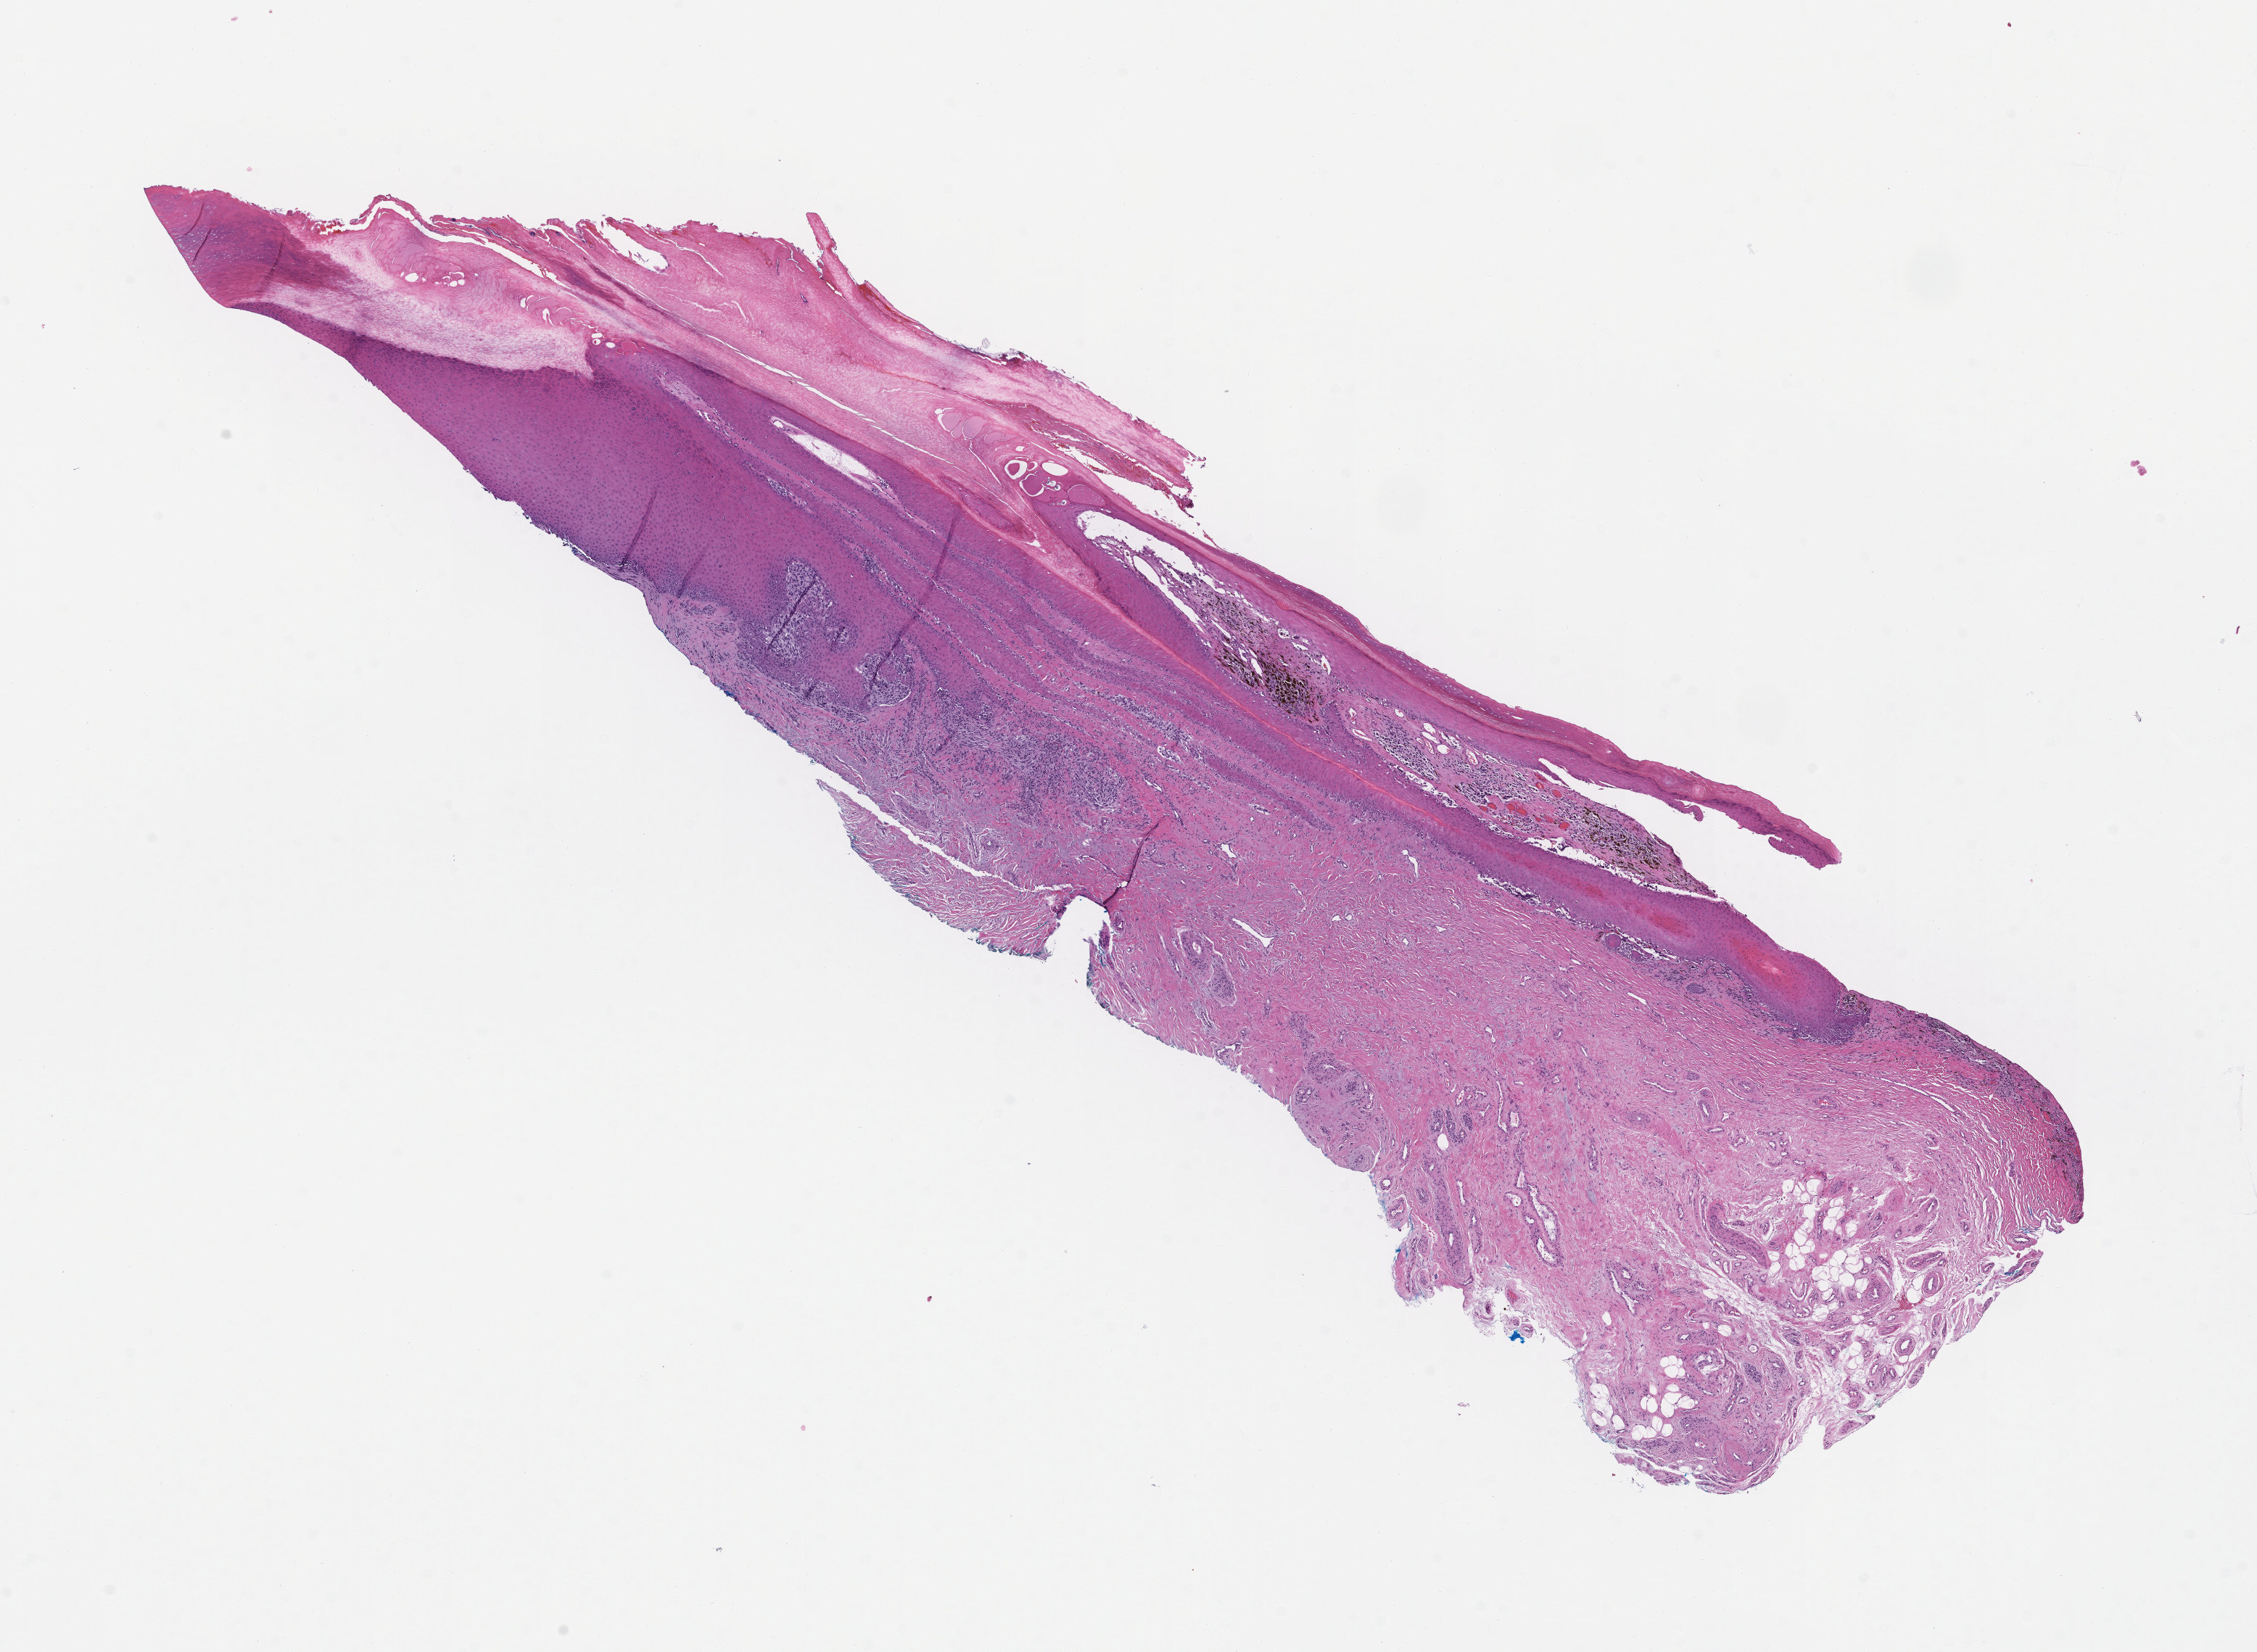
Whole-slide image, haematoxylin and eosin stain, whole scanned area (about 12.6 x 9.2 mm) shown as a low-resolution overview; formalin-fixed, paraffin-embedded (FFPE) tissue; tissue site: skin; specimen time point: archival tissue. Patient: male.
• this section: primary tumor
• diagnosis: Melanoma